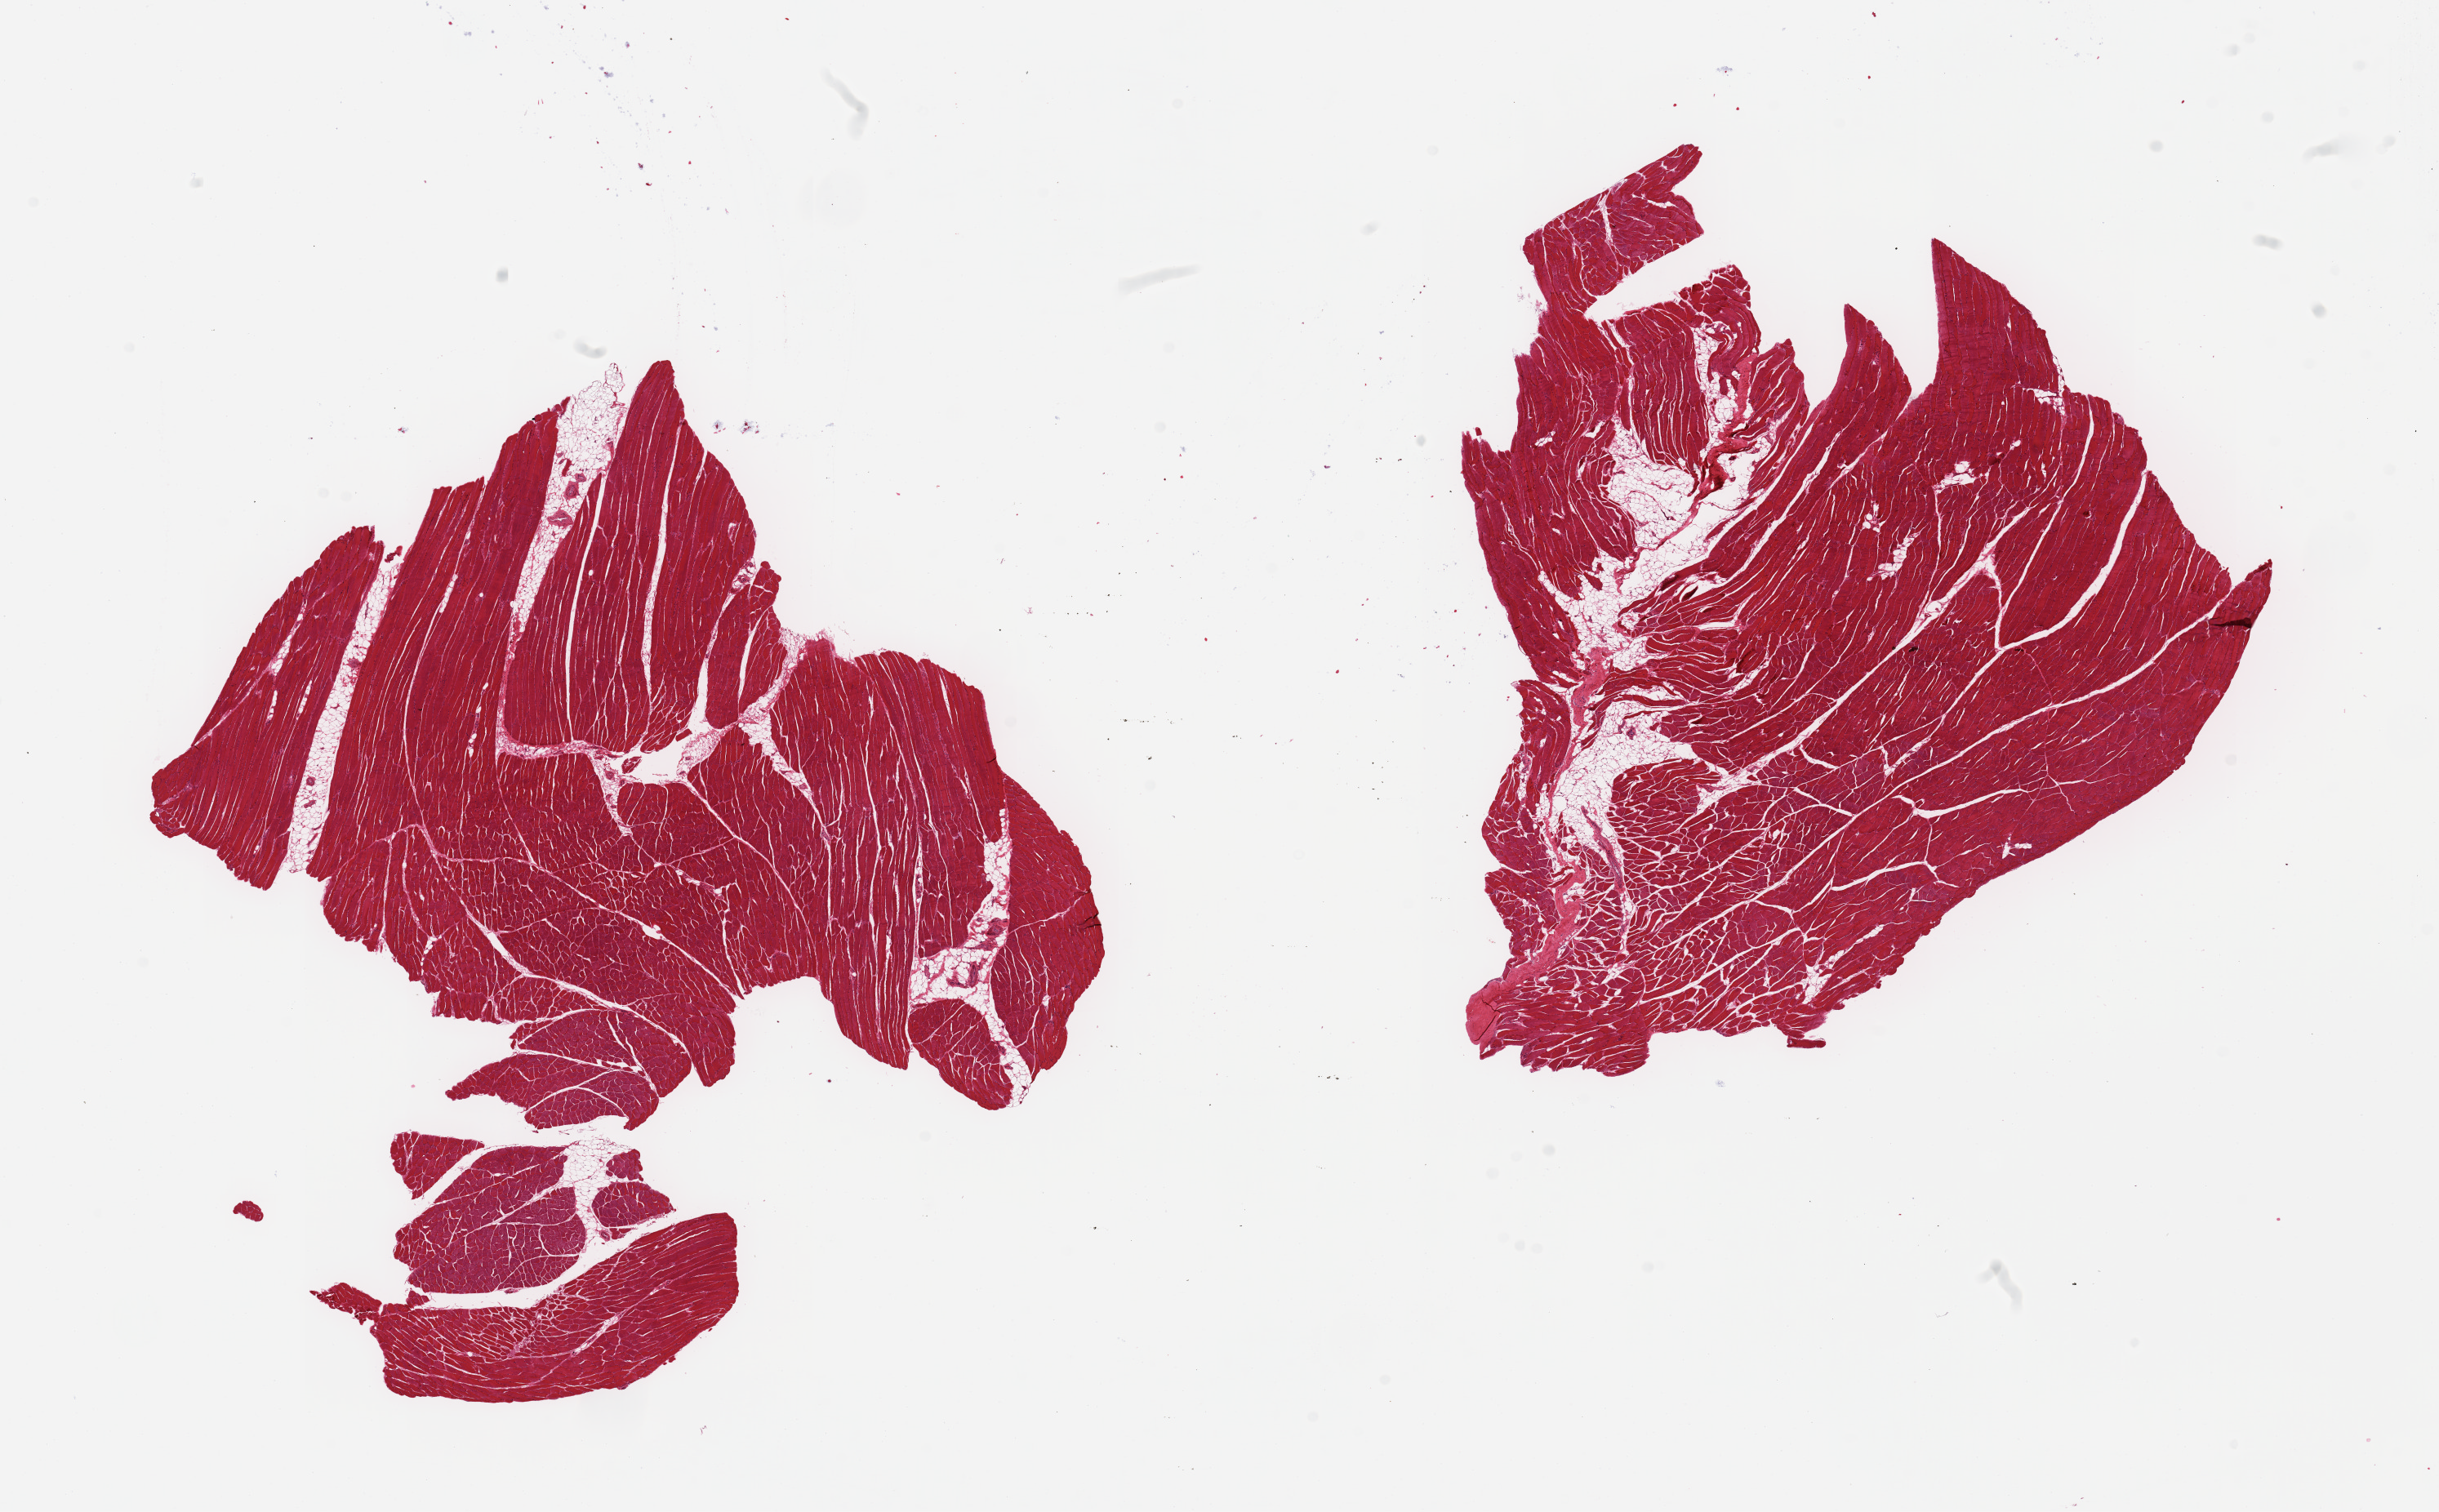
Digitized H&E-stained section — low-resolution overview of the scanned area, about 23.6 x 14.6 mm (acquisition: 20x scan), PAXgene-fixed paraffin-embedded (PFPE) section, target tissue: skeletal muscle, donor tissue sample. Female donor.
Pathologist's review note for this sample: 2 pieces; includes from 5-10% internal fat.